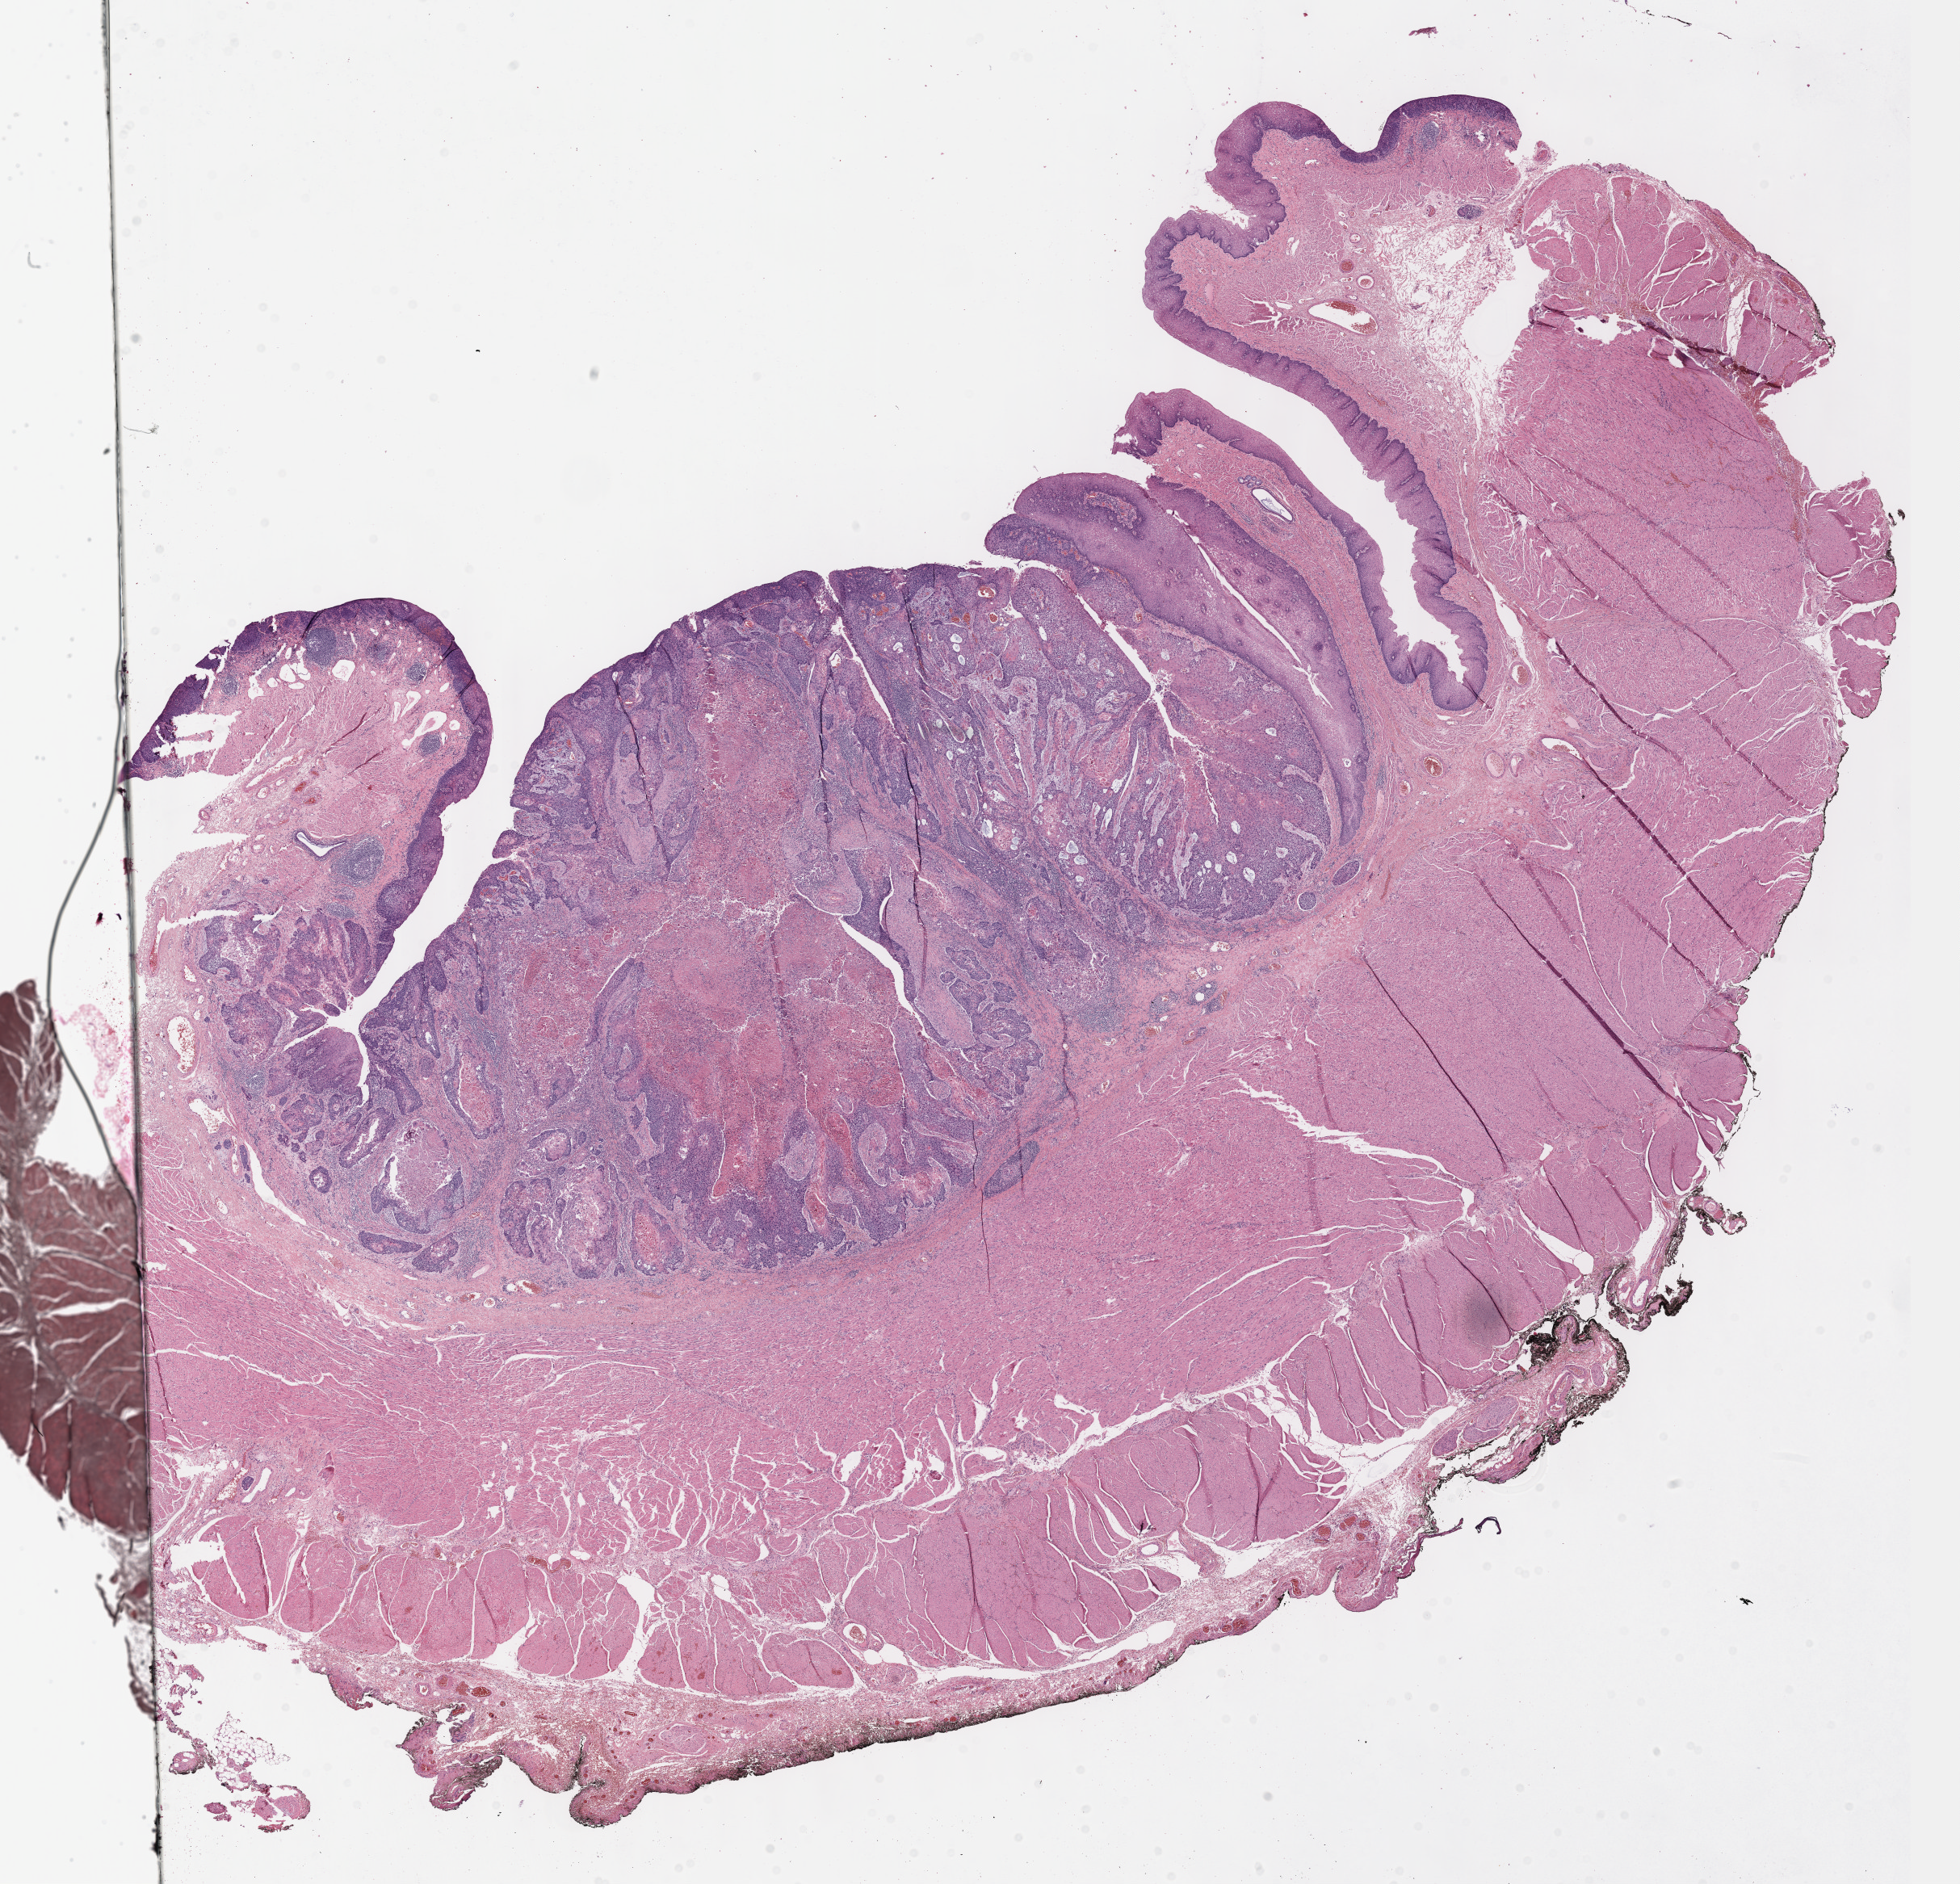
Digitized Hematoxylin and eosin (H&E) stained tissue section (whole slide), whole scanned area (about 19.6 x 18.9 mm, acquisition: 40x scan) shown as a low-resolution overview. Formalin-fixed paraffin-embedded (FFPE) diagnostic section. Esophagus, primary tumour sample. Patient: male, age at initial diagnosis 57 years. Histologic grade: G2 (moderately differentiated).
Pathologic diagnosis: Squamous cell carcinoma, NOS (middle third of esophagus). AJCC pathologic stage: IIIB (7th edition). Lymph nodes positive (case pathology): 4 of 13 examined.